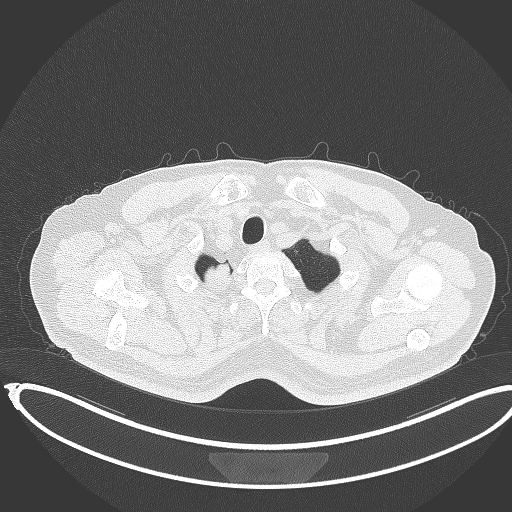
Chest CT, one axial slice. Reconstruction kernel B70f. 120 kVp. Lung window (W 1500 / L -600 HU). 512 × 512 image matrix, field of view 436 × 436 mm. Male patient, age 68 years. From the clinical record (not read from this slice): clinical TNM (as recorded): T2a N0 M0.
Structures marked on this image (rectangle marked by the reading radiologist):
- lung tumour (recorded histology: adenocarcinoma): bounding box [x1, y1, x2, y2] px = [202, 255, 233, 287]